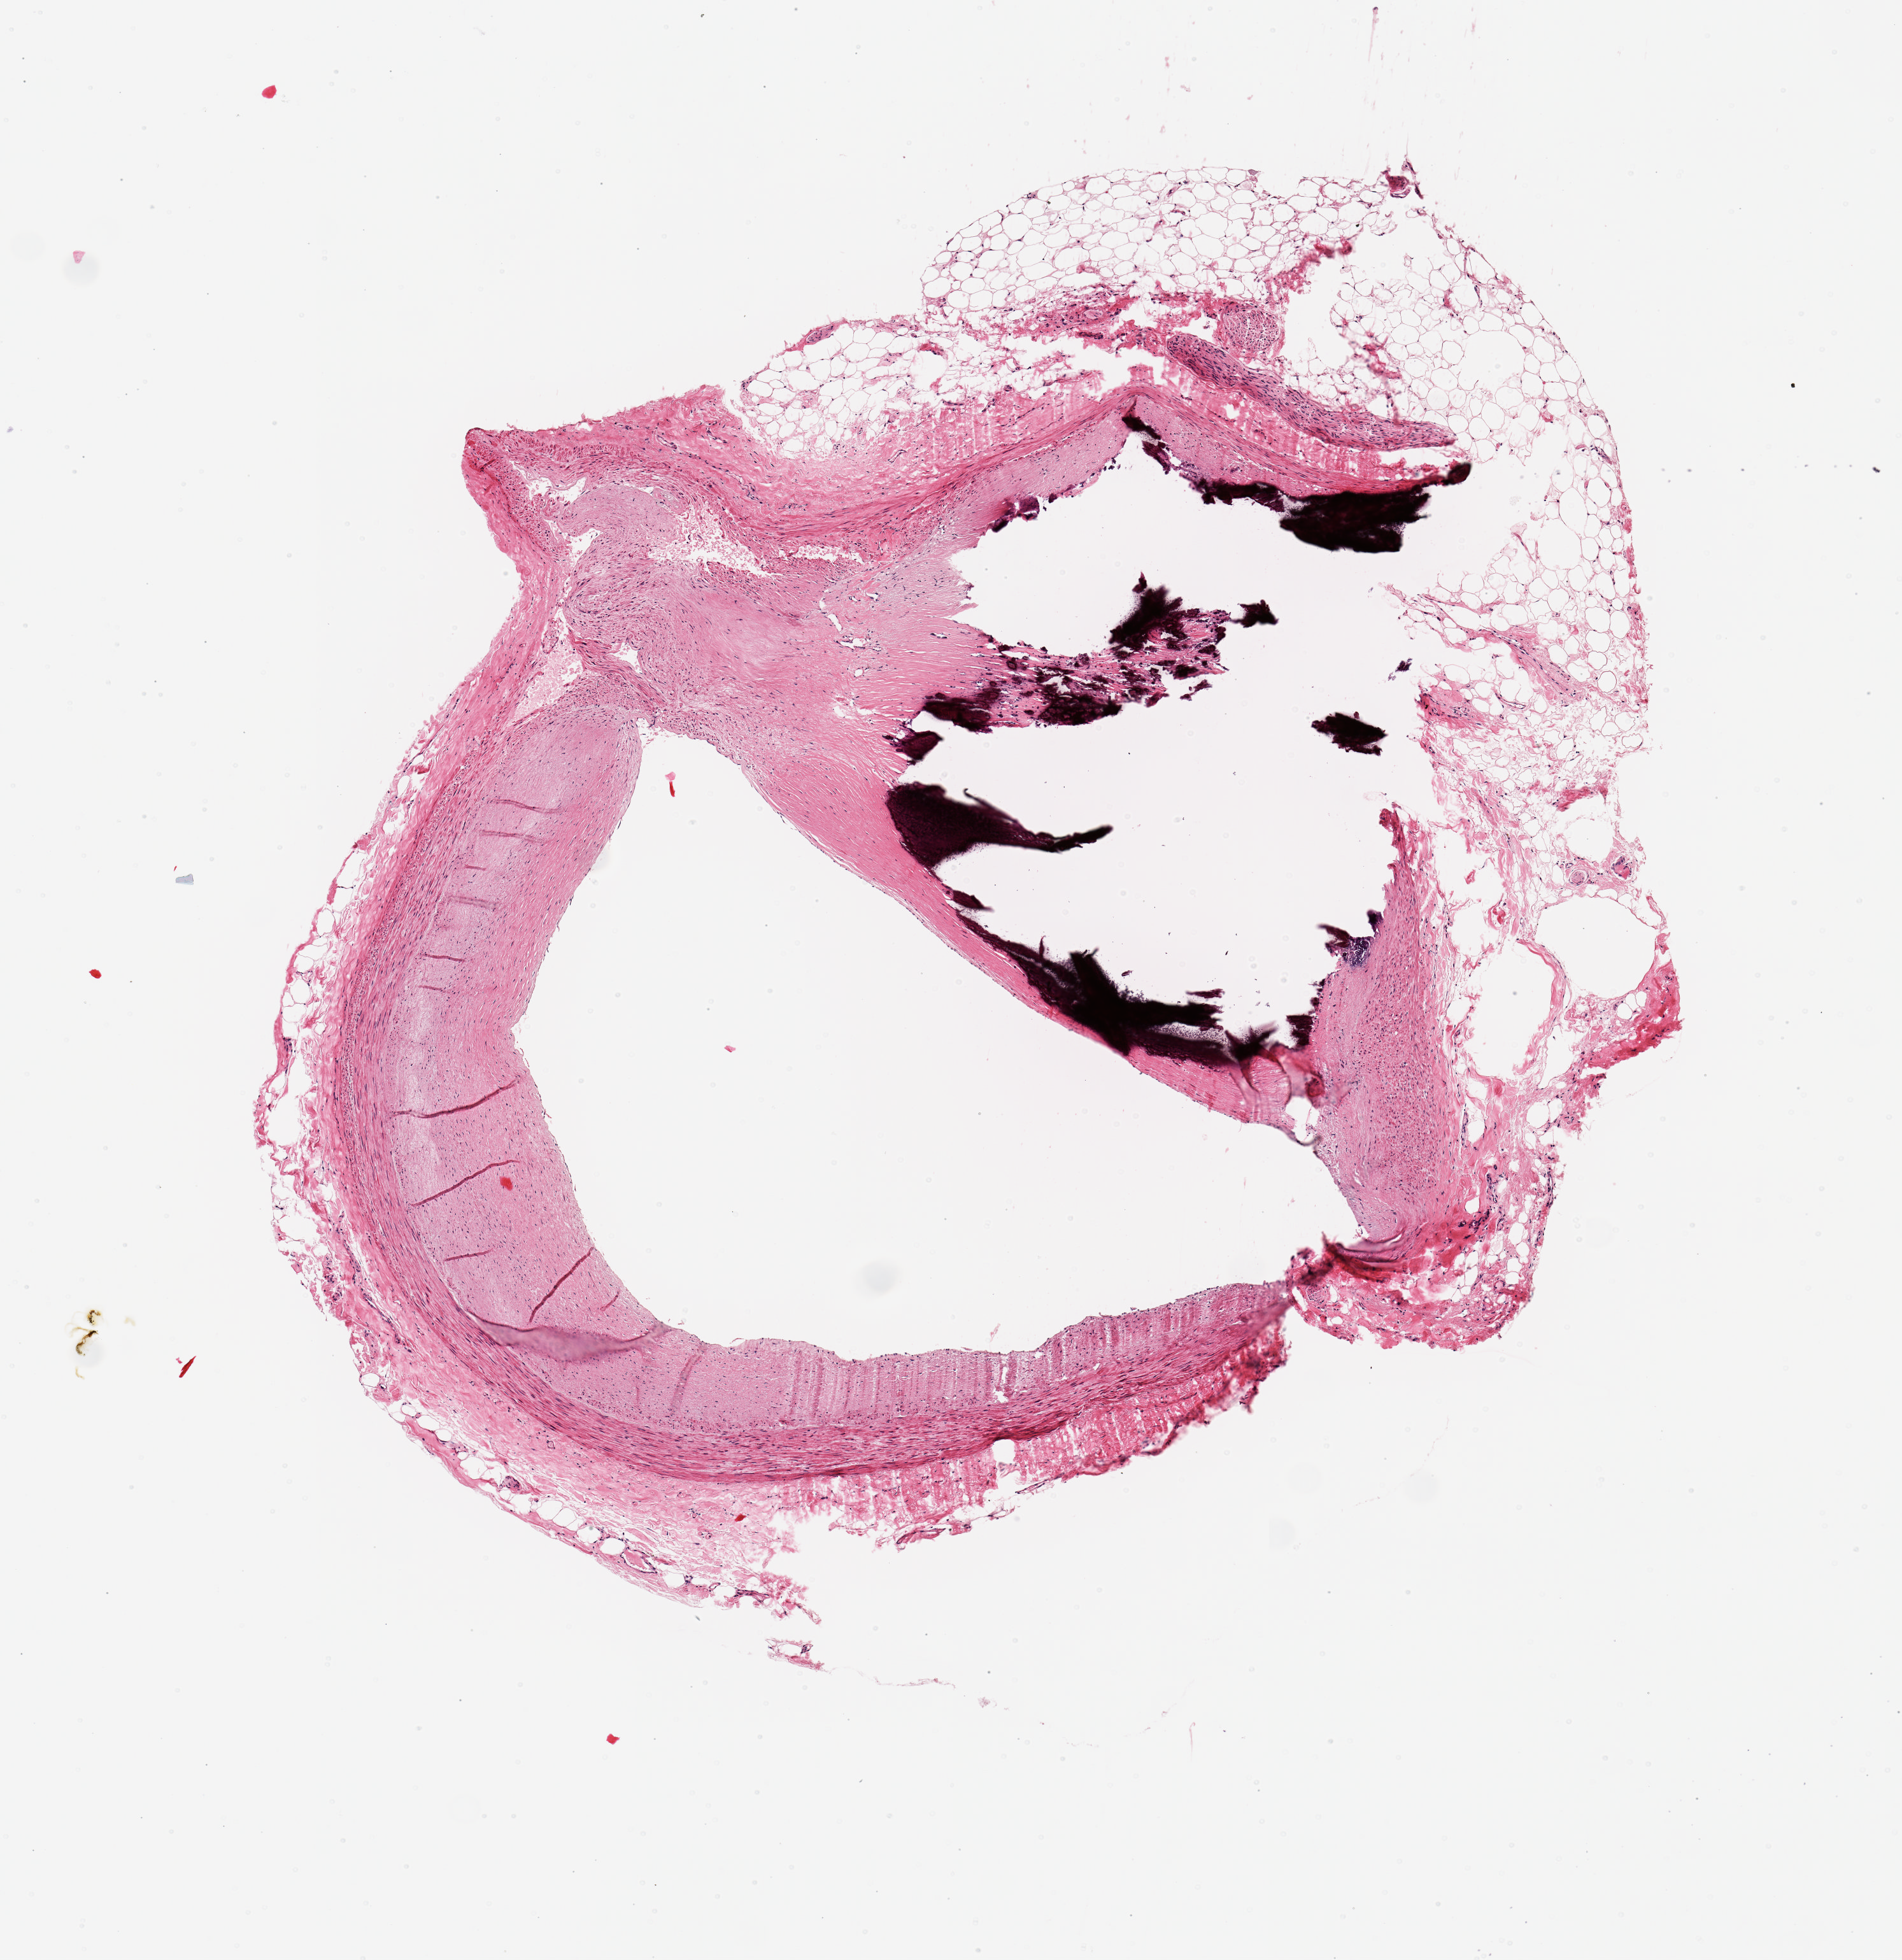
Whole-slide image, H&E stain — low-resolution overview of the scanned area, about 5.9 x 6.1 mm. PAXgene-fixed, paraffin-embedded tissue. Target tissue: coronary artery. Tissue donor sample.
Reviewer comment on this tissue sample: 1 piece; large eccentric calcified plaque occludes 50%; perivascular fat up to 0.6 mm thick.